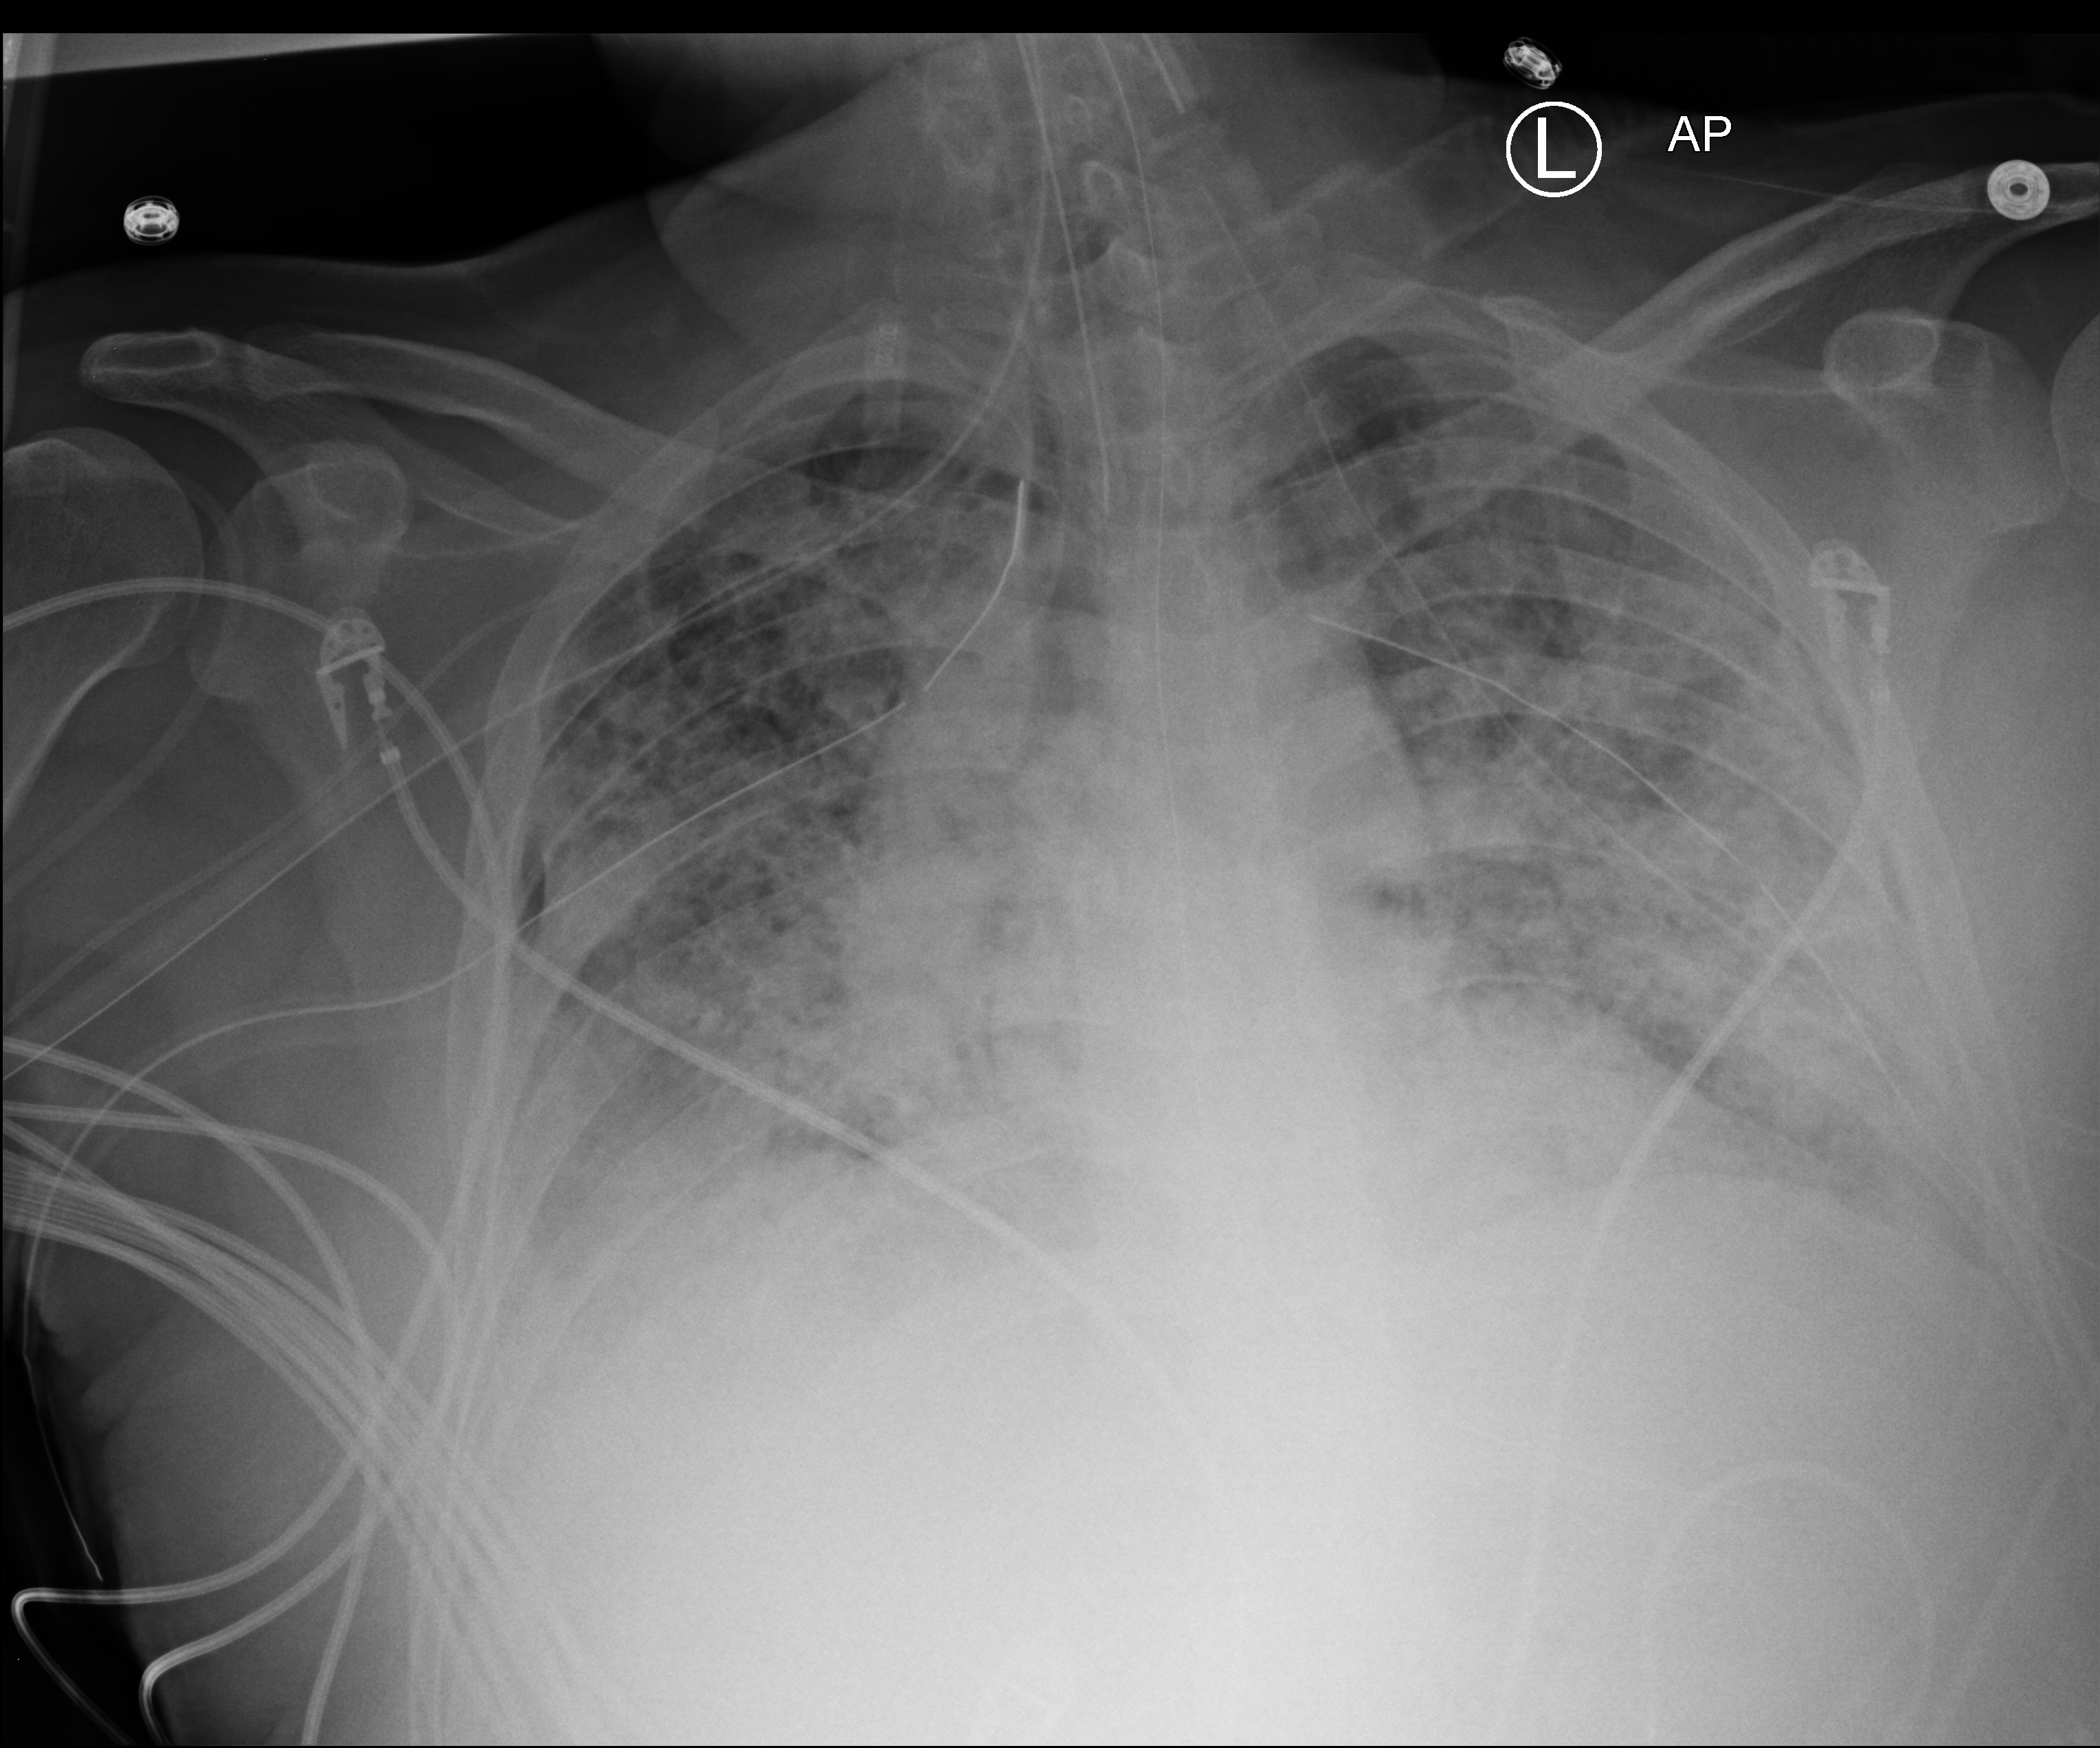
Chest X-ray (portable). Patient hospitalised with COVID-19; male, aged 18–59 years.
Admission-level facts for this patient (not findings on this image; timing relative to this image not recorded):
- length of hospital stay: 63 days